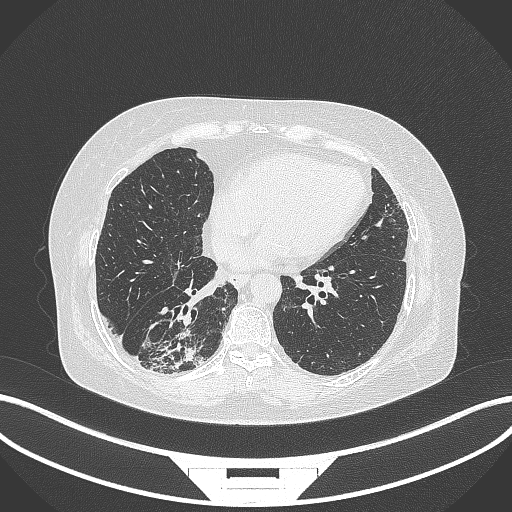
Chest CT, one axial slice. Reconstruction kernel B70f. Lung window (W 1500 / L -600 HU). 1 mm slice thickness. 512 × 512 image matrix, field of view 400 × 400 mm. Patient: female, 65 years. From the clinical record (not read from this slice): clinical TNM (as recorded): T2b N1 M0; histopathological grade: G1.
Outlined on this slice (rectangle marked by the reading radiologist):
- lung tumour (recorded histology: adenocarcinoma): box from (x=134, y=313) to (x=202, y=378) px